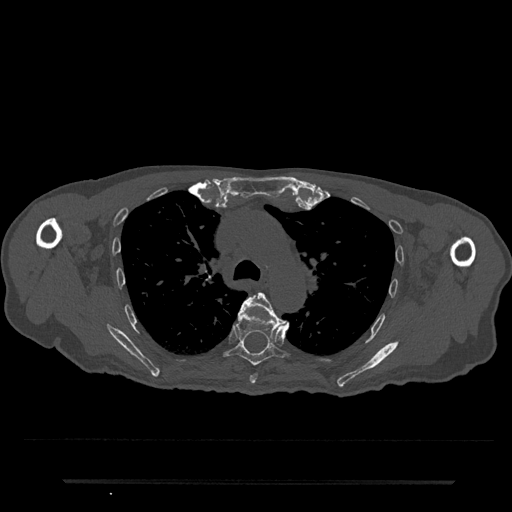
CT including the spine, one axial slice; slice 542 of 797 in the series (ordered by position); reconstruction kernel Br40s/3; 120 kVp; bone window (W 1800 / L 400 HU); 0.5 mm slice thickness; 512 × 512 image matrix. Patient: male, 74 years. Case-level facts recorded for this patient, not image findings: primary cancer: prostate.
Annotated regions visible in this slice (semi-automatic segmentation, software-assisted and operator-edited):
- T5 vertebra: bounding box (x1, y1, x2, y2) in pixels: (239, 292, 289, 384)
- T6 vertebra: (224, 298, 291, 366)